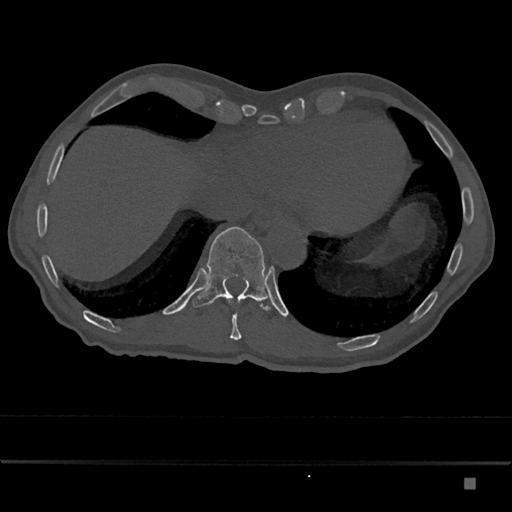
CT including the spine, one axial slice; position 699 of 797 along the scan axis; reconstruction kernel Br40s/3; 120 kVp; bone window (W 1800 / L 400 HU); 0.5 mm slice thickness; 512 × 512 image matrix. Male patient, age 72 years. Case-level facts recorded for this patient, not image findings: primary cancer: prostate.
Structures marked on this image (semi-automatically segmented with operator editing):
- T10 vertebra: box from (x=228, y=298) to (x=242, y=340) px
- T11 vertebra: (x=192, y=227)–(x=271, y=311)